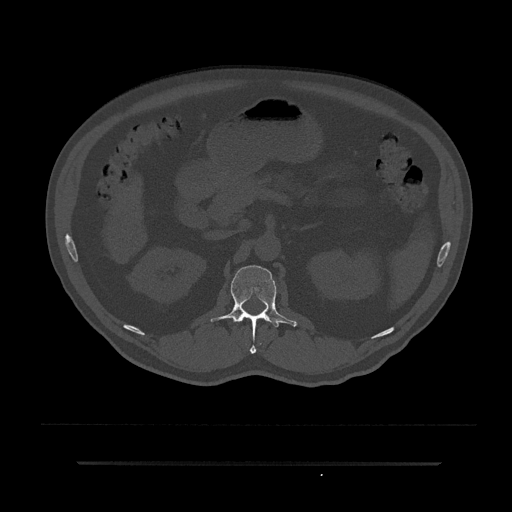
CT including the spine, one axial slice; position 149 of 797 along the scan axis; reconstruction kernel Br40s/3; bone window (W 1800 / L 400 HU); 0.5 mm slice thickness; 512 × 512 image matrix, field of view 464 × 464 mm. Male patient, age 59 years. From the clinical record (not read from this slice): primary cancer: bile ducts; vertebrae with lytic lesions (as recorded): T10.
Outlined on this slice (semi-automatically segmented with operator editing):
- L1 vertebra: bounding box (x1, y1, x2, y2) in pixels: (210, 265, 297, 354)